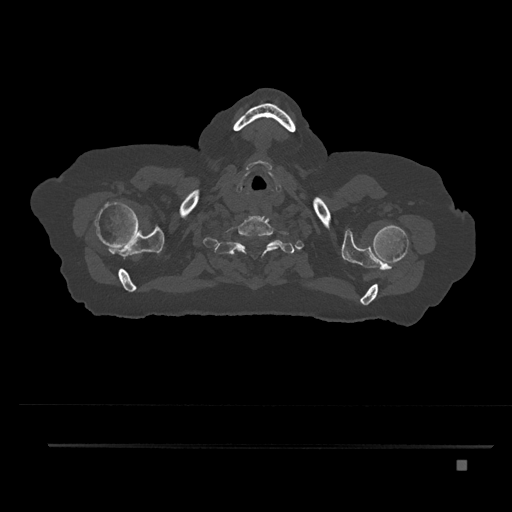
CT including the spine, one axial slice. Slice 713 of 797 in the series (ordered by position). Reconstruction kernel Br40s/3. Bone window (W 1800 / L 400 HU). 512 × 512 image matrix. Female patient, age 76 years. Case-level facts recorded for this patient, not image findings: primary cancer: lung.
Annotated regions visible in this slice (semi-automatically segmented with operator editing):
- T1 vertebra: box from (x=223, y=240) to (x=282, y=257) px